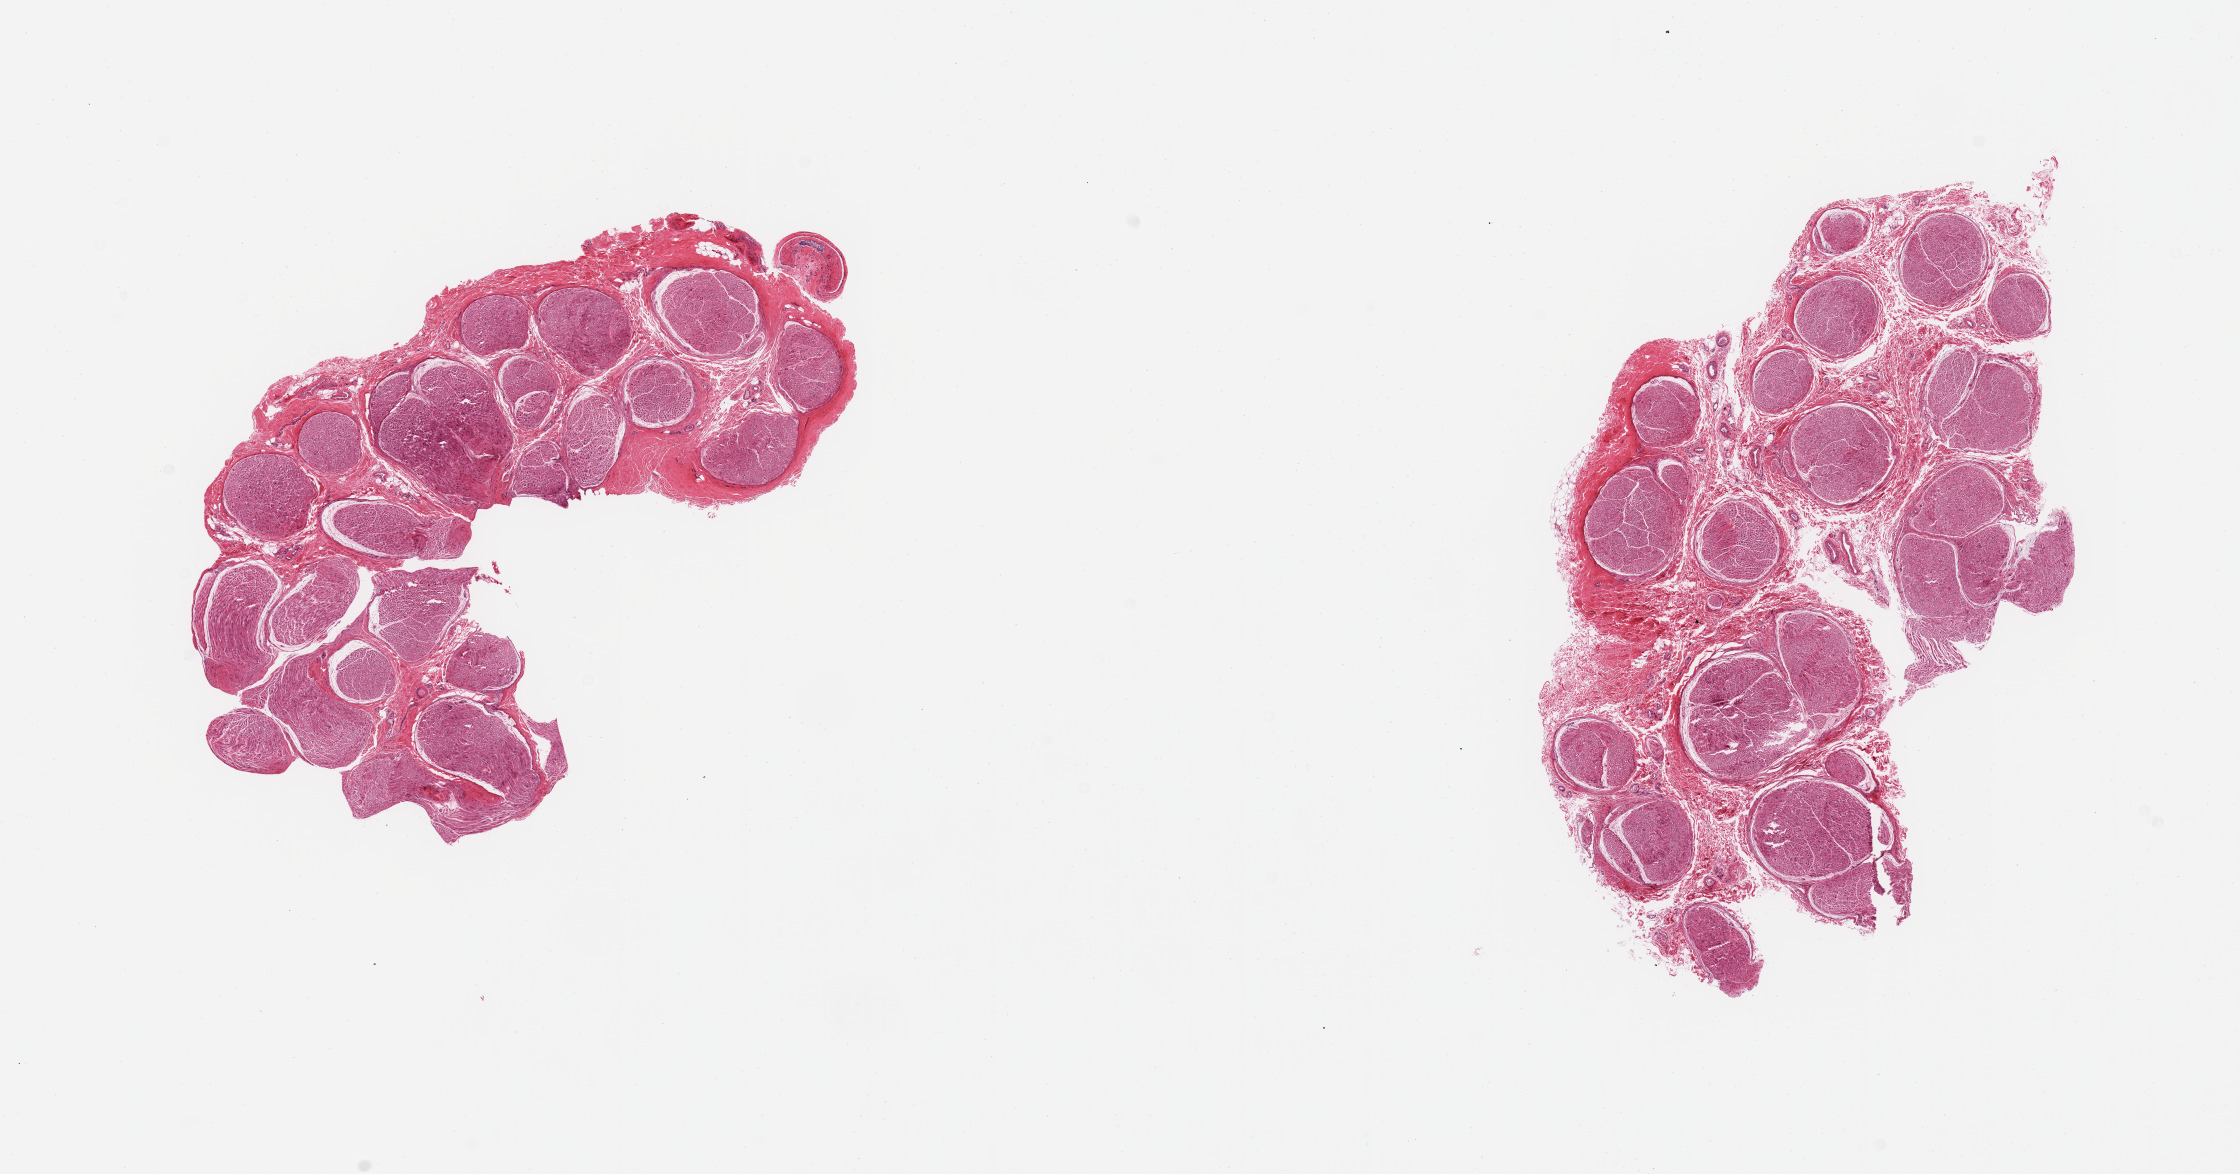
Hematoxylin and eosin (H&E) whole-slide image, shown as a low-resolution overview of the whole scanned area (about 17.7 x 9.3 mm, acquisition: 20x scan); PAXgene-fixed, paraffin-embedded tissue; target tissue: tibial nerve; tissue donor sample. Male donor.
* review note (as recorded): 2 pieces; low fat content